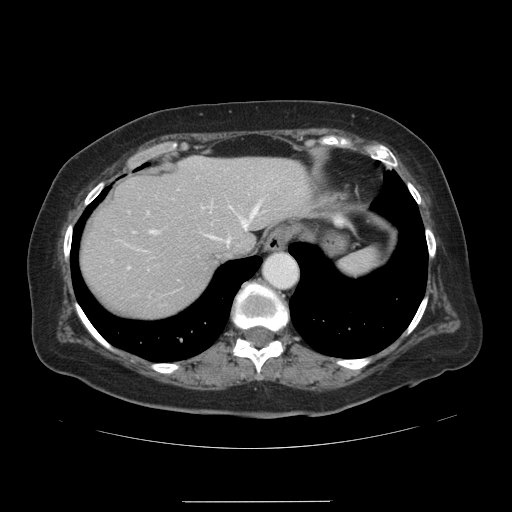
Contrast-enhanced abdominal CT, one axial slice; slice 111 of 141 in the series (ordered by position); soft-tissue window (W 400 / L 40 HU); 512 × 512 image matrix, field of view 393 × 393 mm. Female patient, age 74 years. From the clinical record (not read from this slice): diagnosis: colorectal cancer liver metastases, imaged before liver resection; multiple liver metastases: yes; largest metastasis: 7 cm; chemotherapy before resection: no.
Structures marked on this image (manually delineated by an expert):
- hepatic veins: box from (x=135, y=198) to (x=263, y=252) px
- liver: (x=81, y=157)–(x=315, y=316)
- planned liver remnant (the part of the liver to remain after resection): (x=81, y=157)–(x=315, y=316)
- portal vein (with intrahepatic branches): (x=128, y=214)–(x=252, y=267)